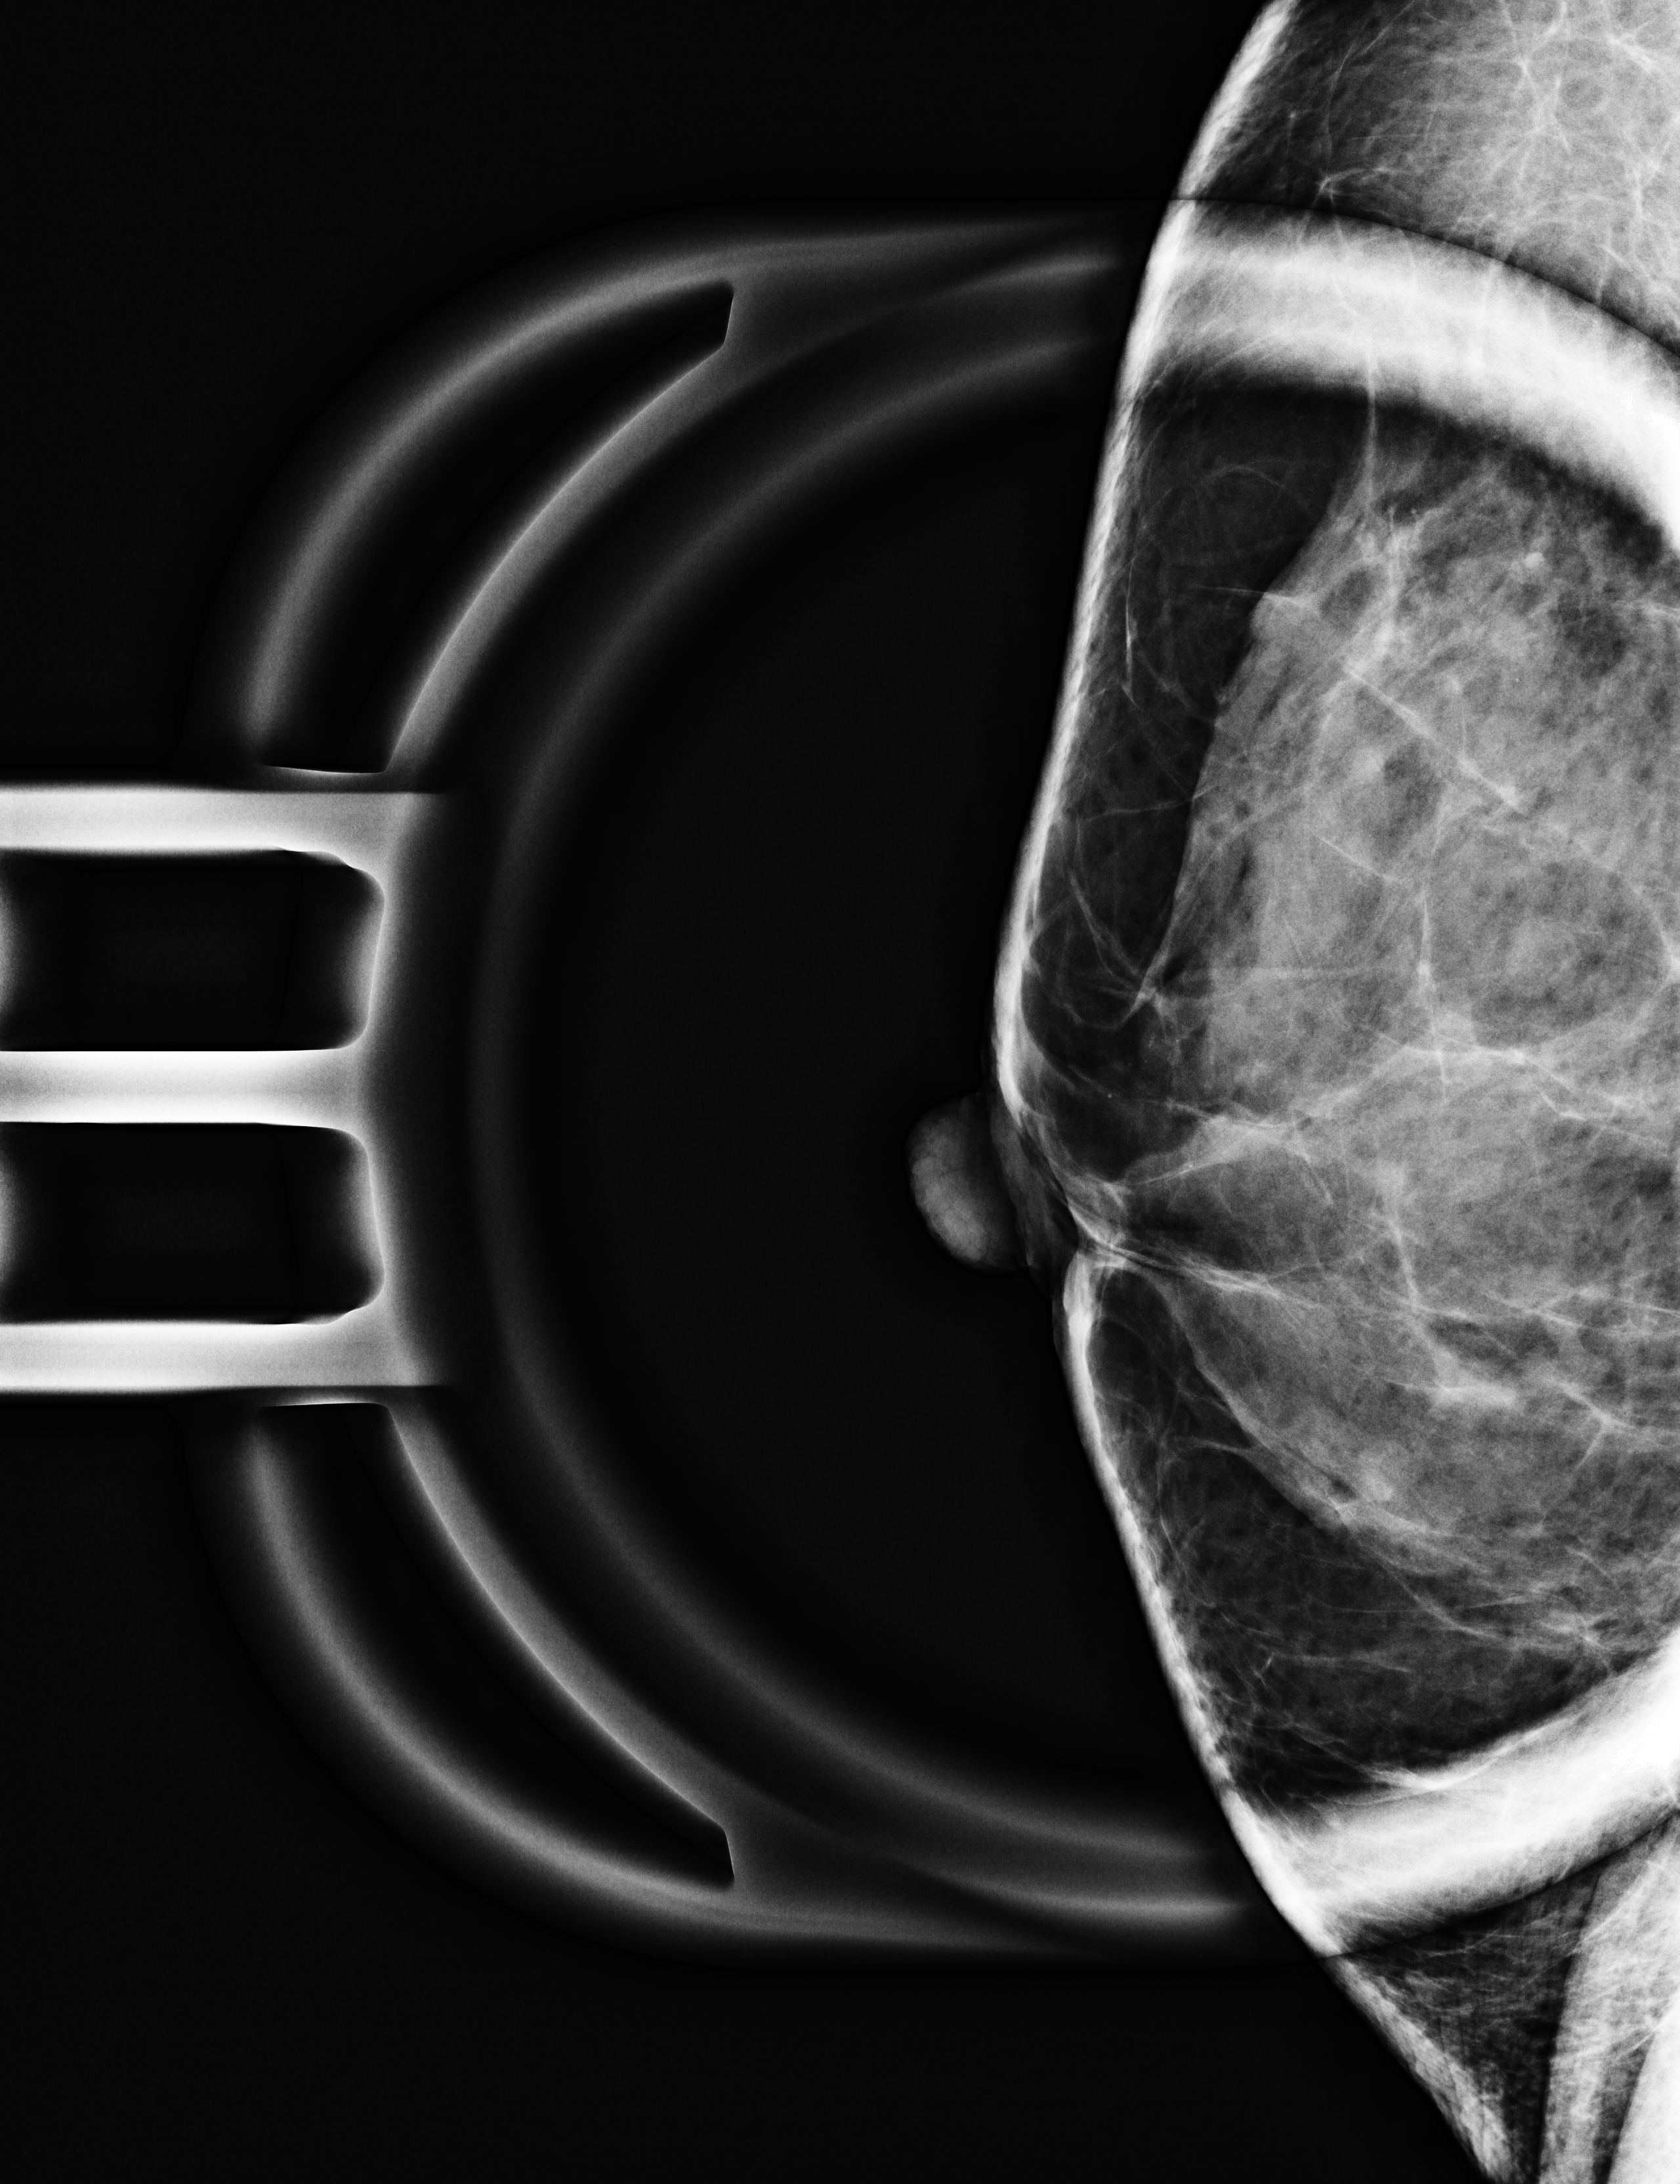
Additional work-up view, compressed breast thickness 26 mm, system: Selenia Dimensions. Patient aged 58 years (female).
Image type: full-field digital mammogram. Breast: right. Projection: ML view, magnification.